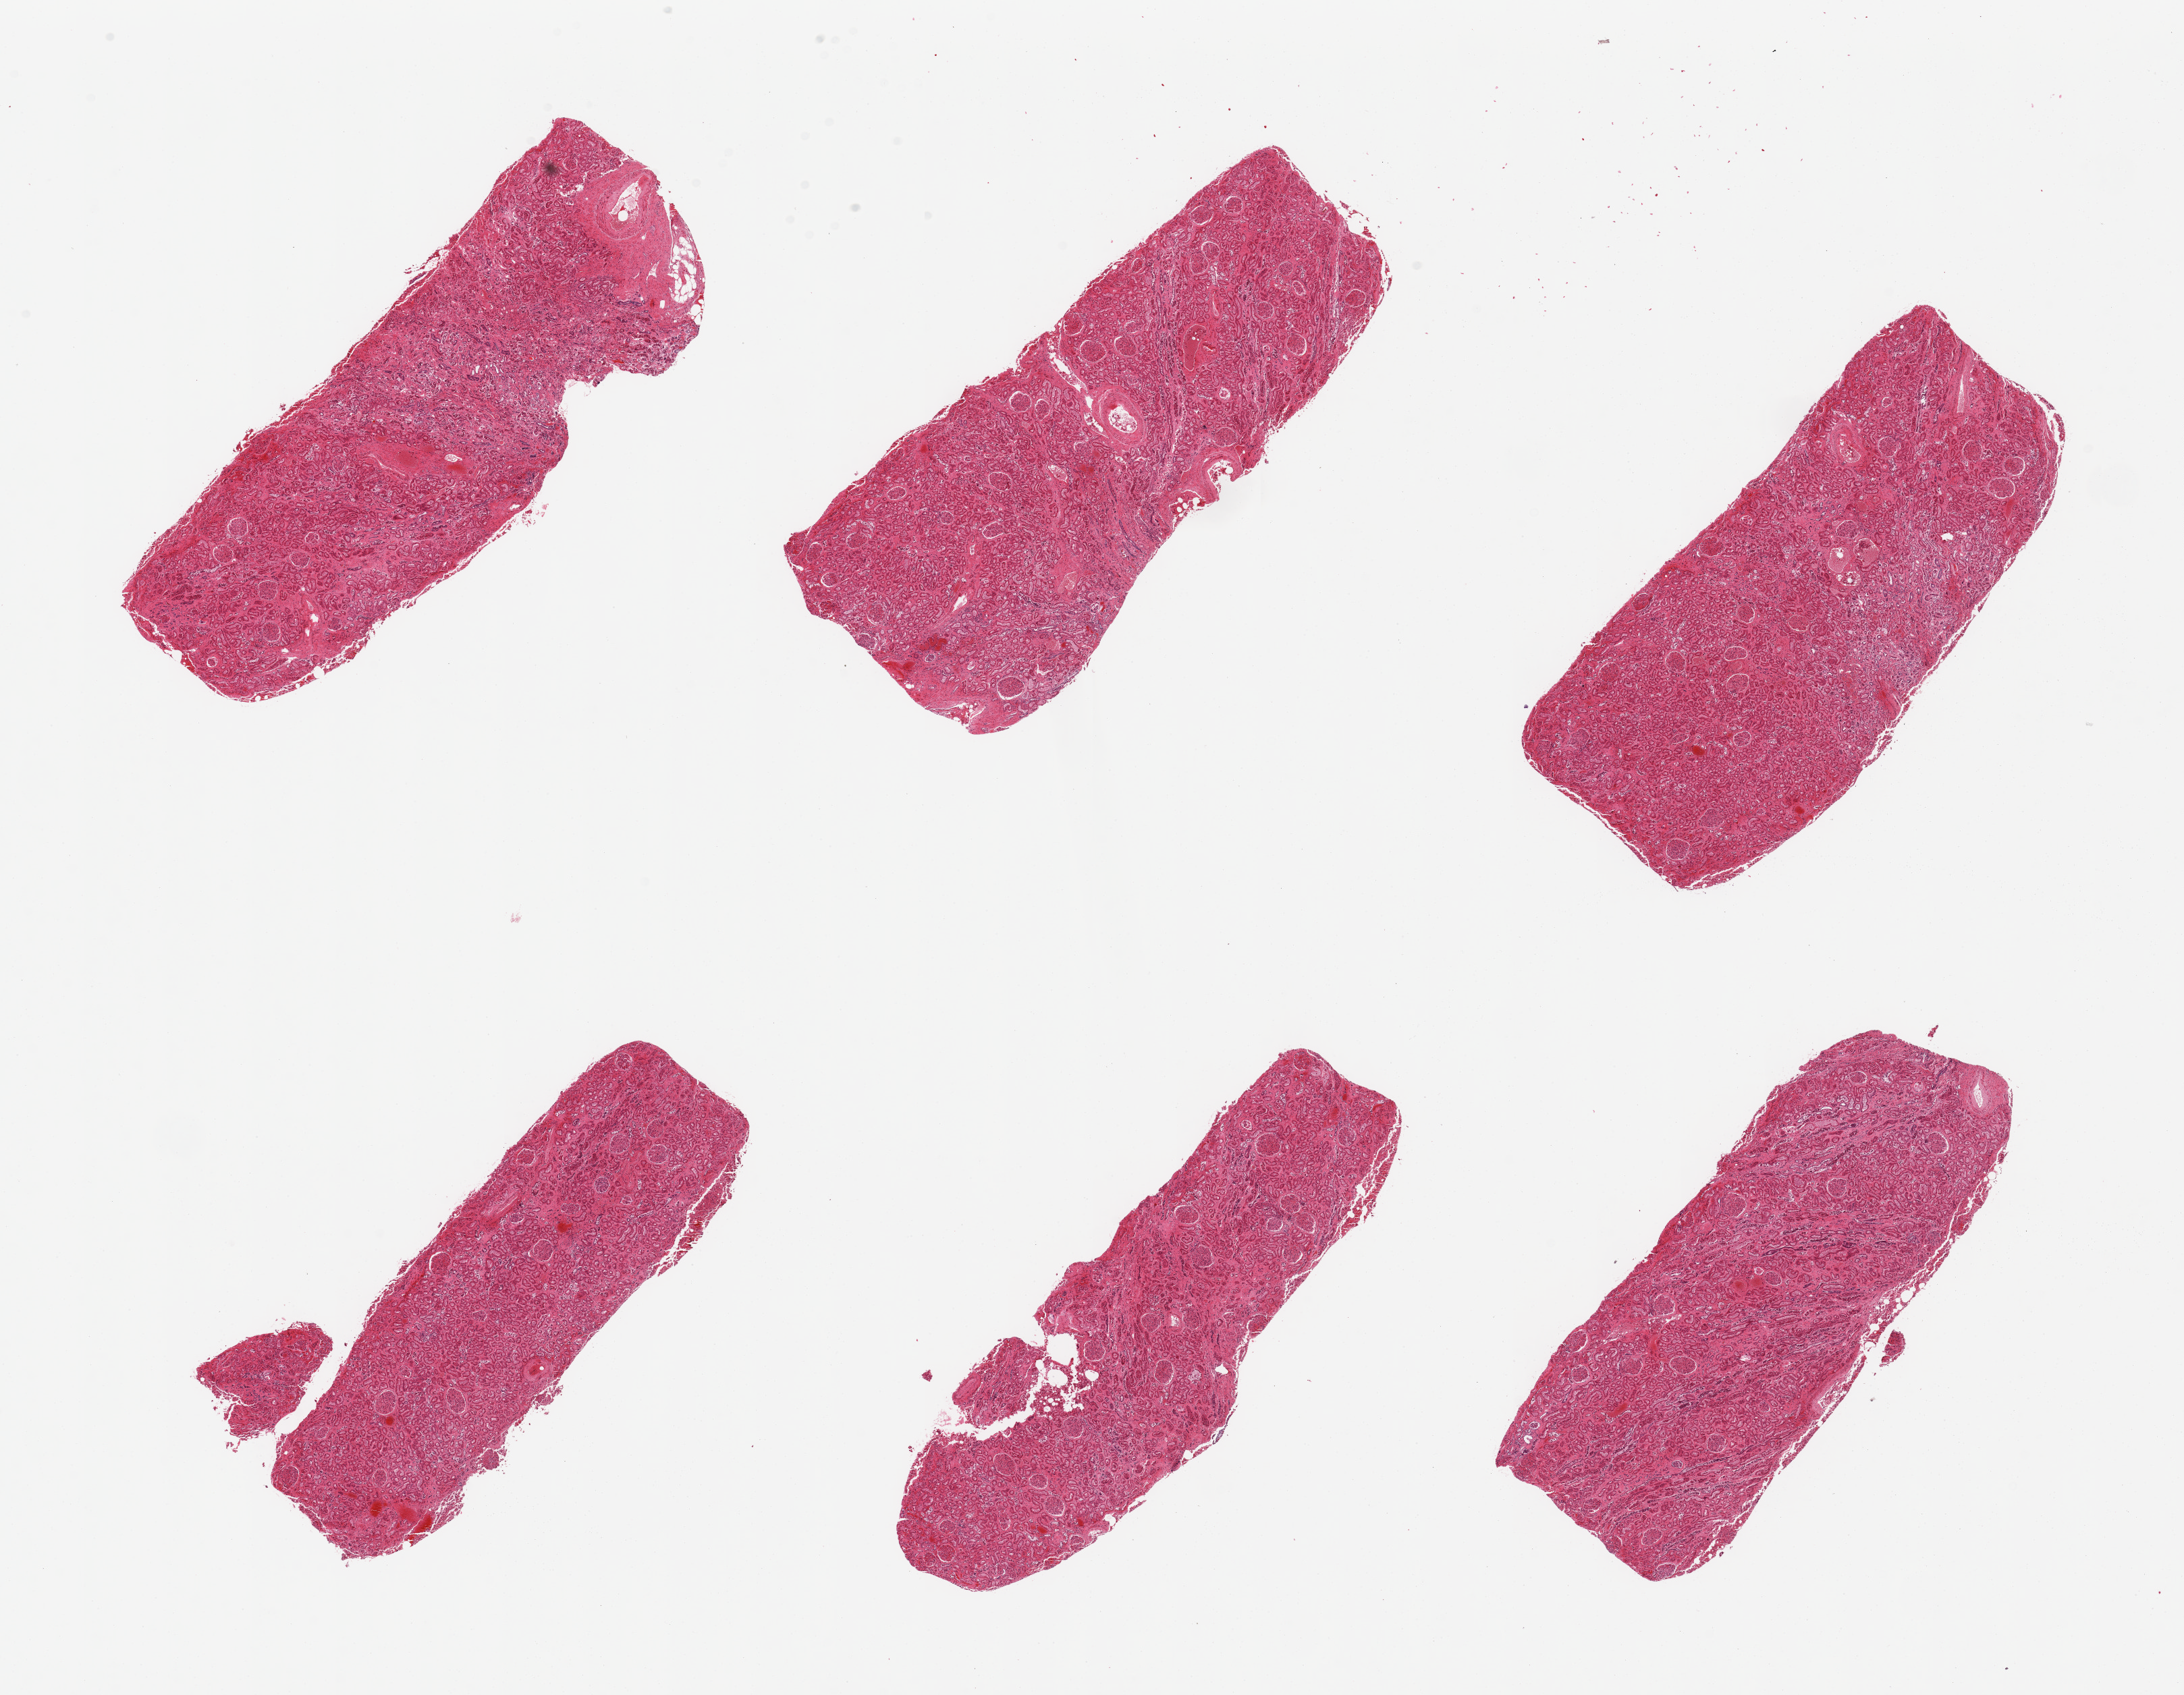
Digitized haematoxylin and eosin-stained section — a low-resolution overview of the entire scanned area, about 25.6 x 19.9 mm (acquisition: 20x scan). PAXgene-fixed, paraffin-embedded tissue. Sampled site (target tissue): renal cortex. Donor tissue sample. Donor: male.
Review note (as recorded): 6 pieces, glomeruli present in all sections.